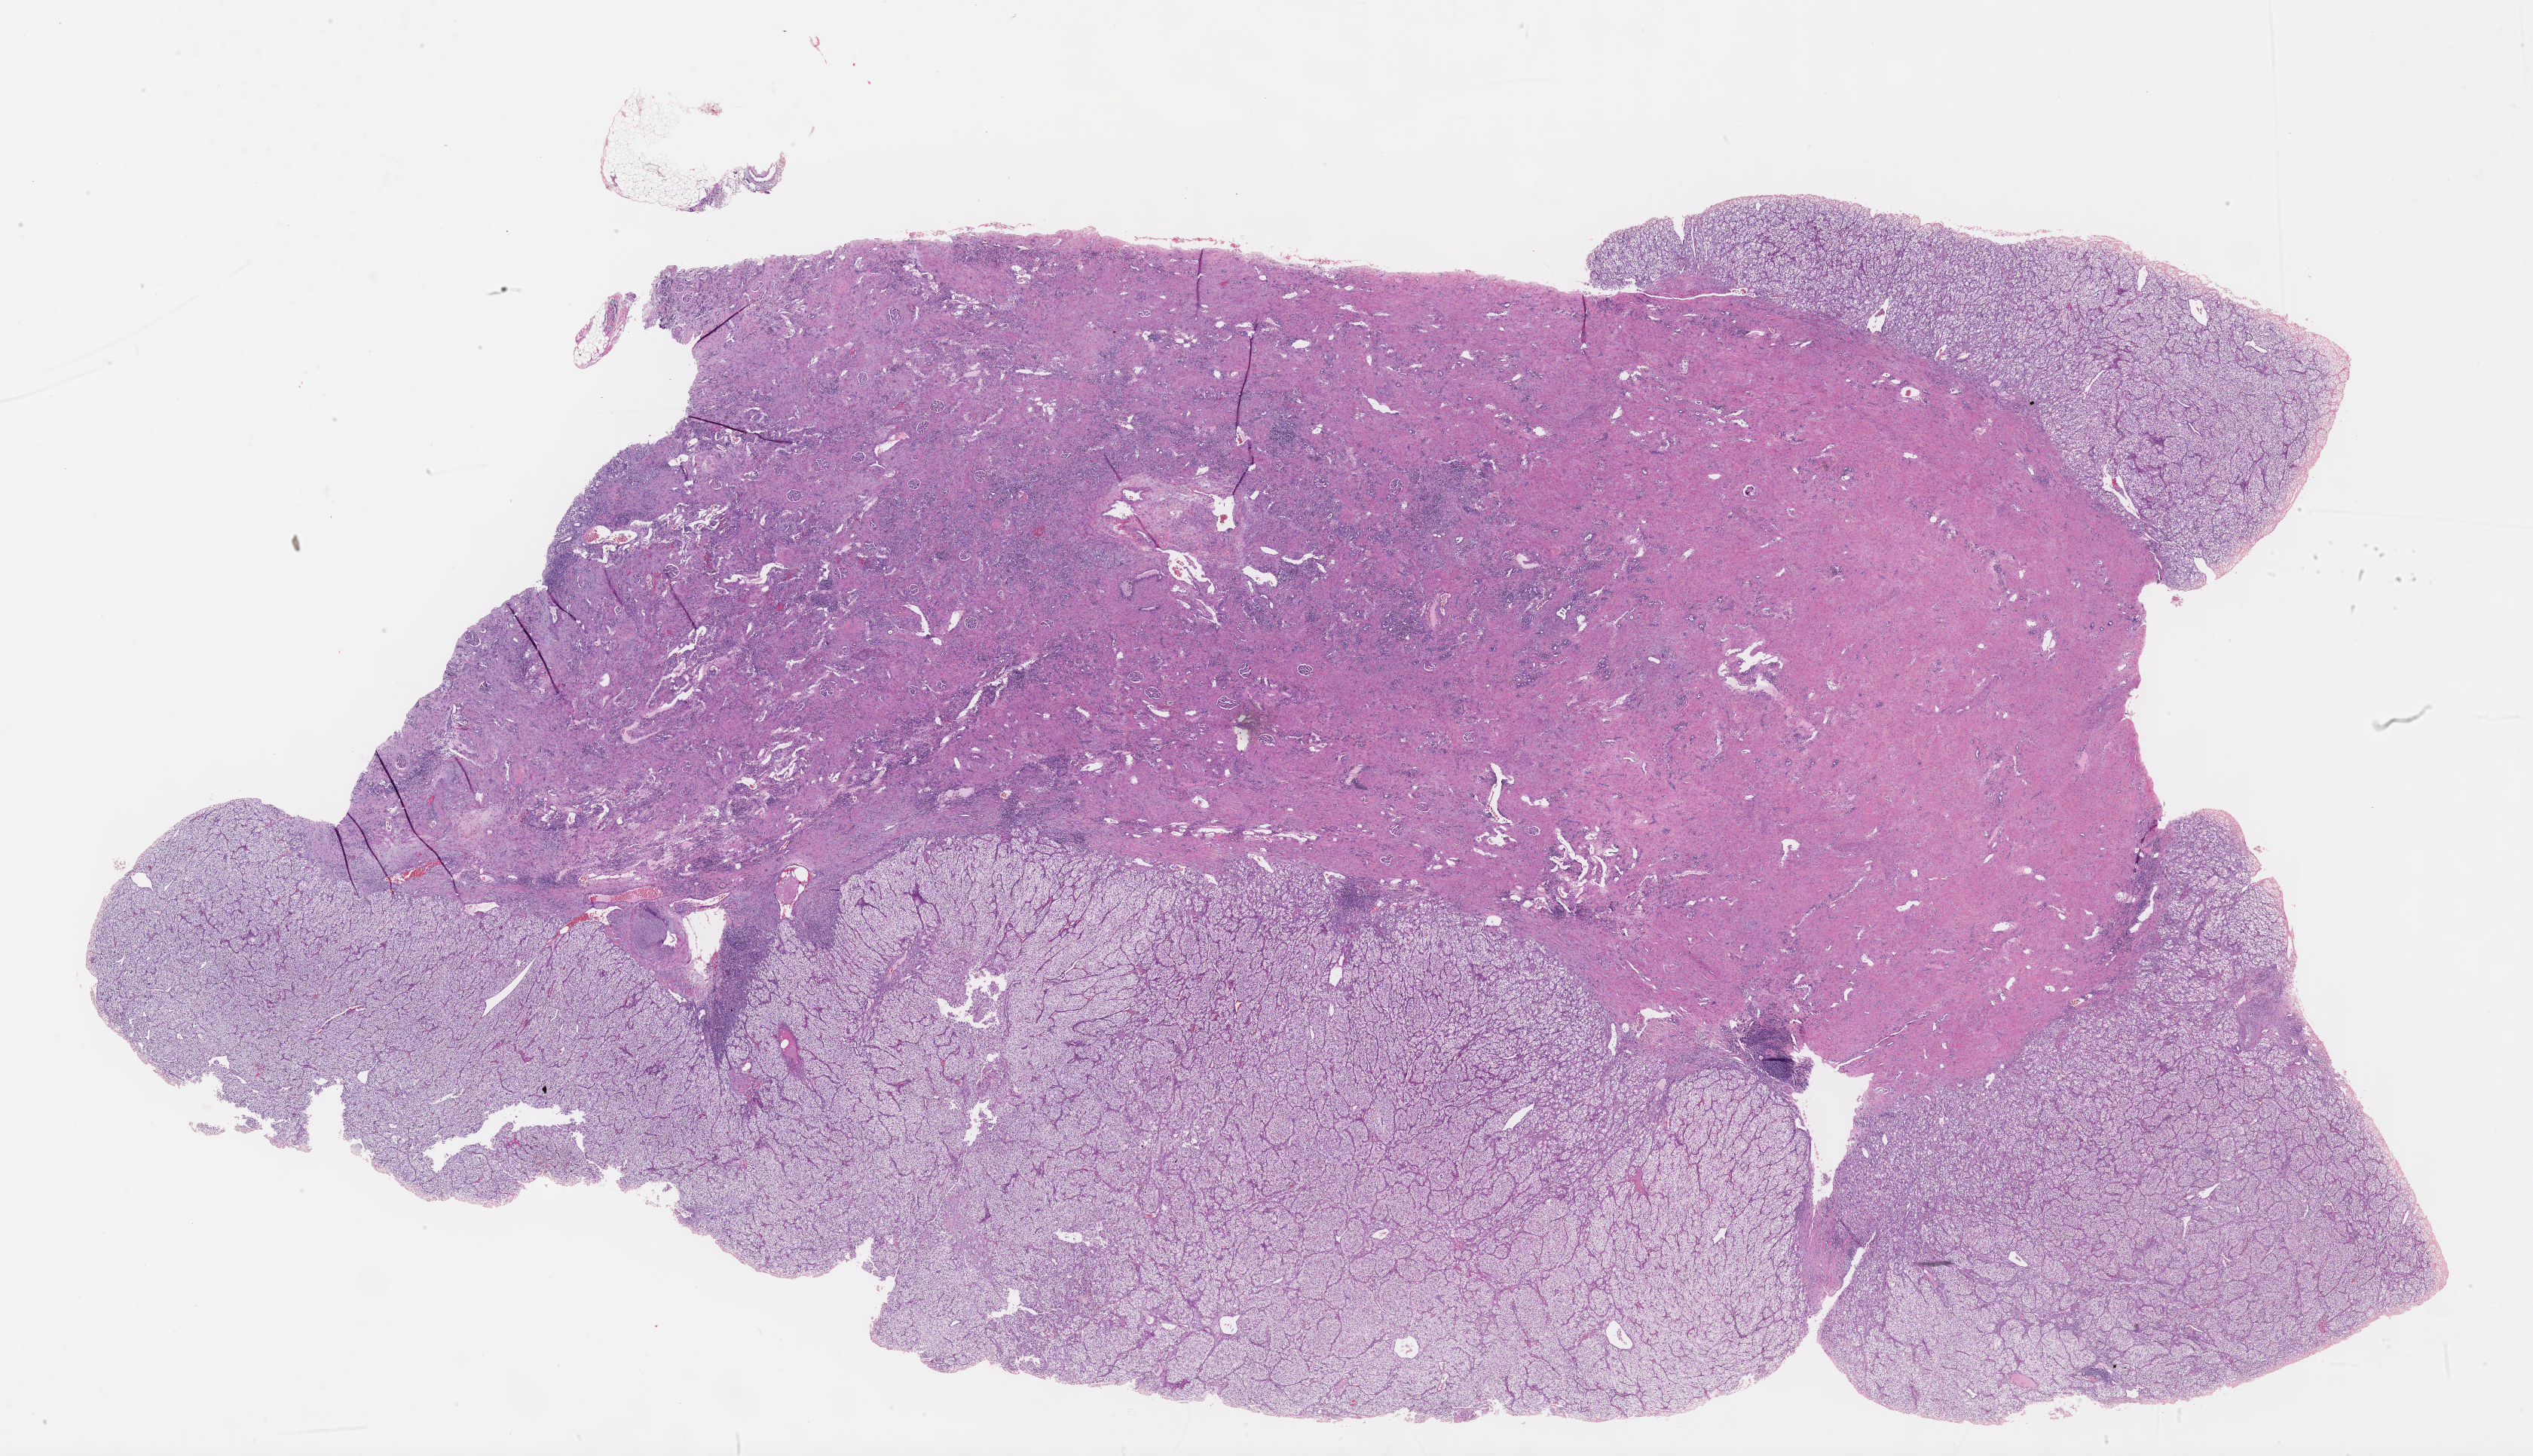
Whole-slide histology image, H&E, low-resolution overview of the scanned area, about 27.2 x 15.6 mm; FFPE section; sample: primary tumour, kidney. Male, age 63 years at initial diagnosis. Histologic grade: G4 (undifferentiated).
AJCC pathologic stage: IV. Diagnosis: Clear cell adenocarcinoma, NOS. Laterality: left.